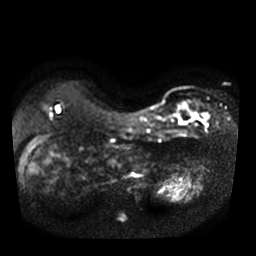
Breast MRI, one axial slice. Diffusion-weighted series; image 2 of 4 stored at this slice position (different b-values; order by instance number). 3 T. 5 mm slice thickness. 256 × 256 image matrix, field of view 320 × 320 mm. Female patient.
Structures marked on this image (expert manual segmentation):
- tumour on diffusion-weighted imaging: bounding box (x1, y1, x2, y2) in pixels: (187, 108, 207, 120)